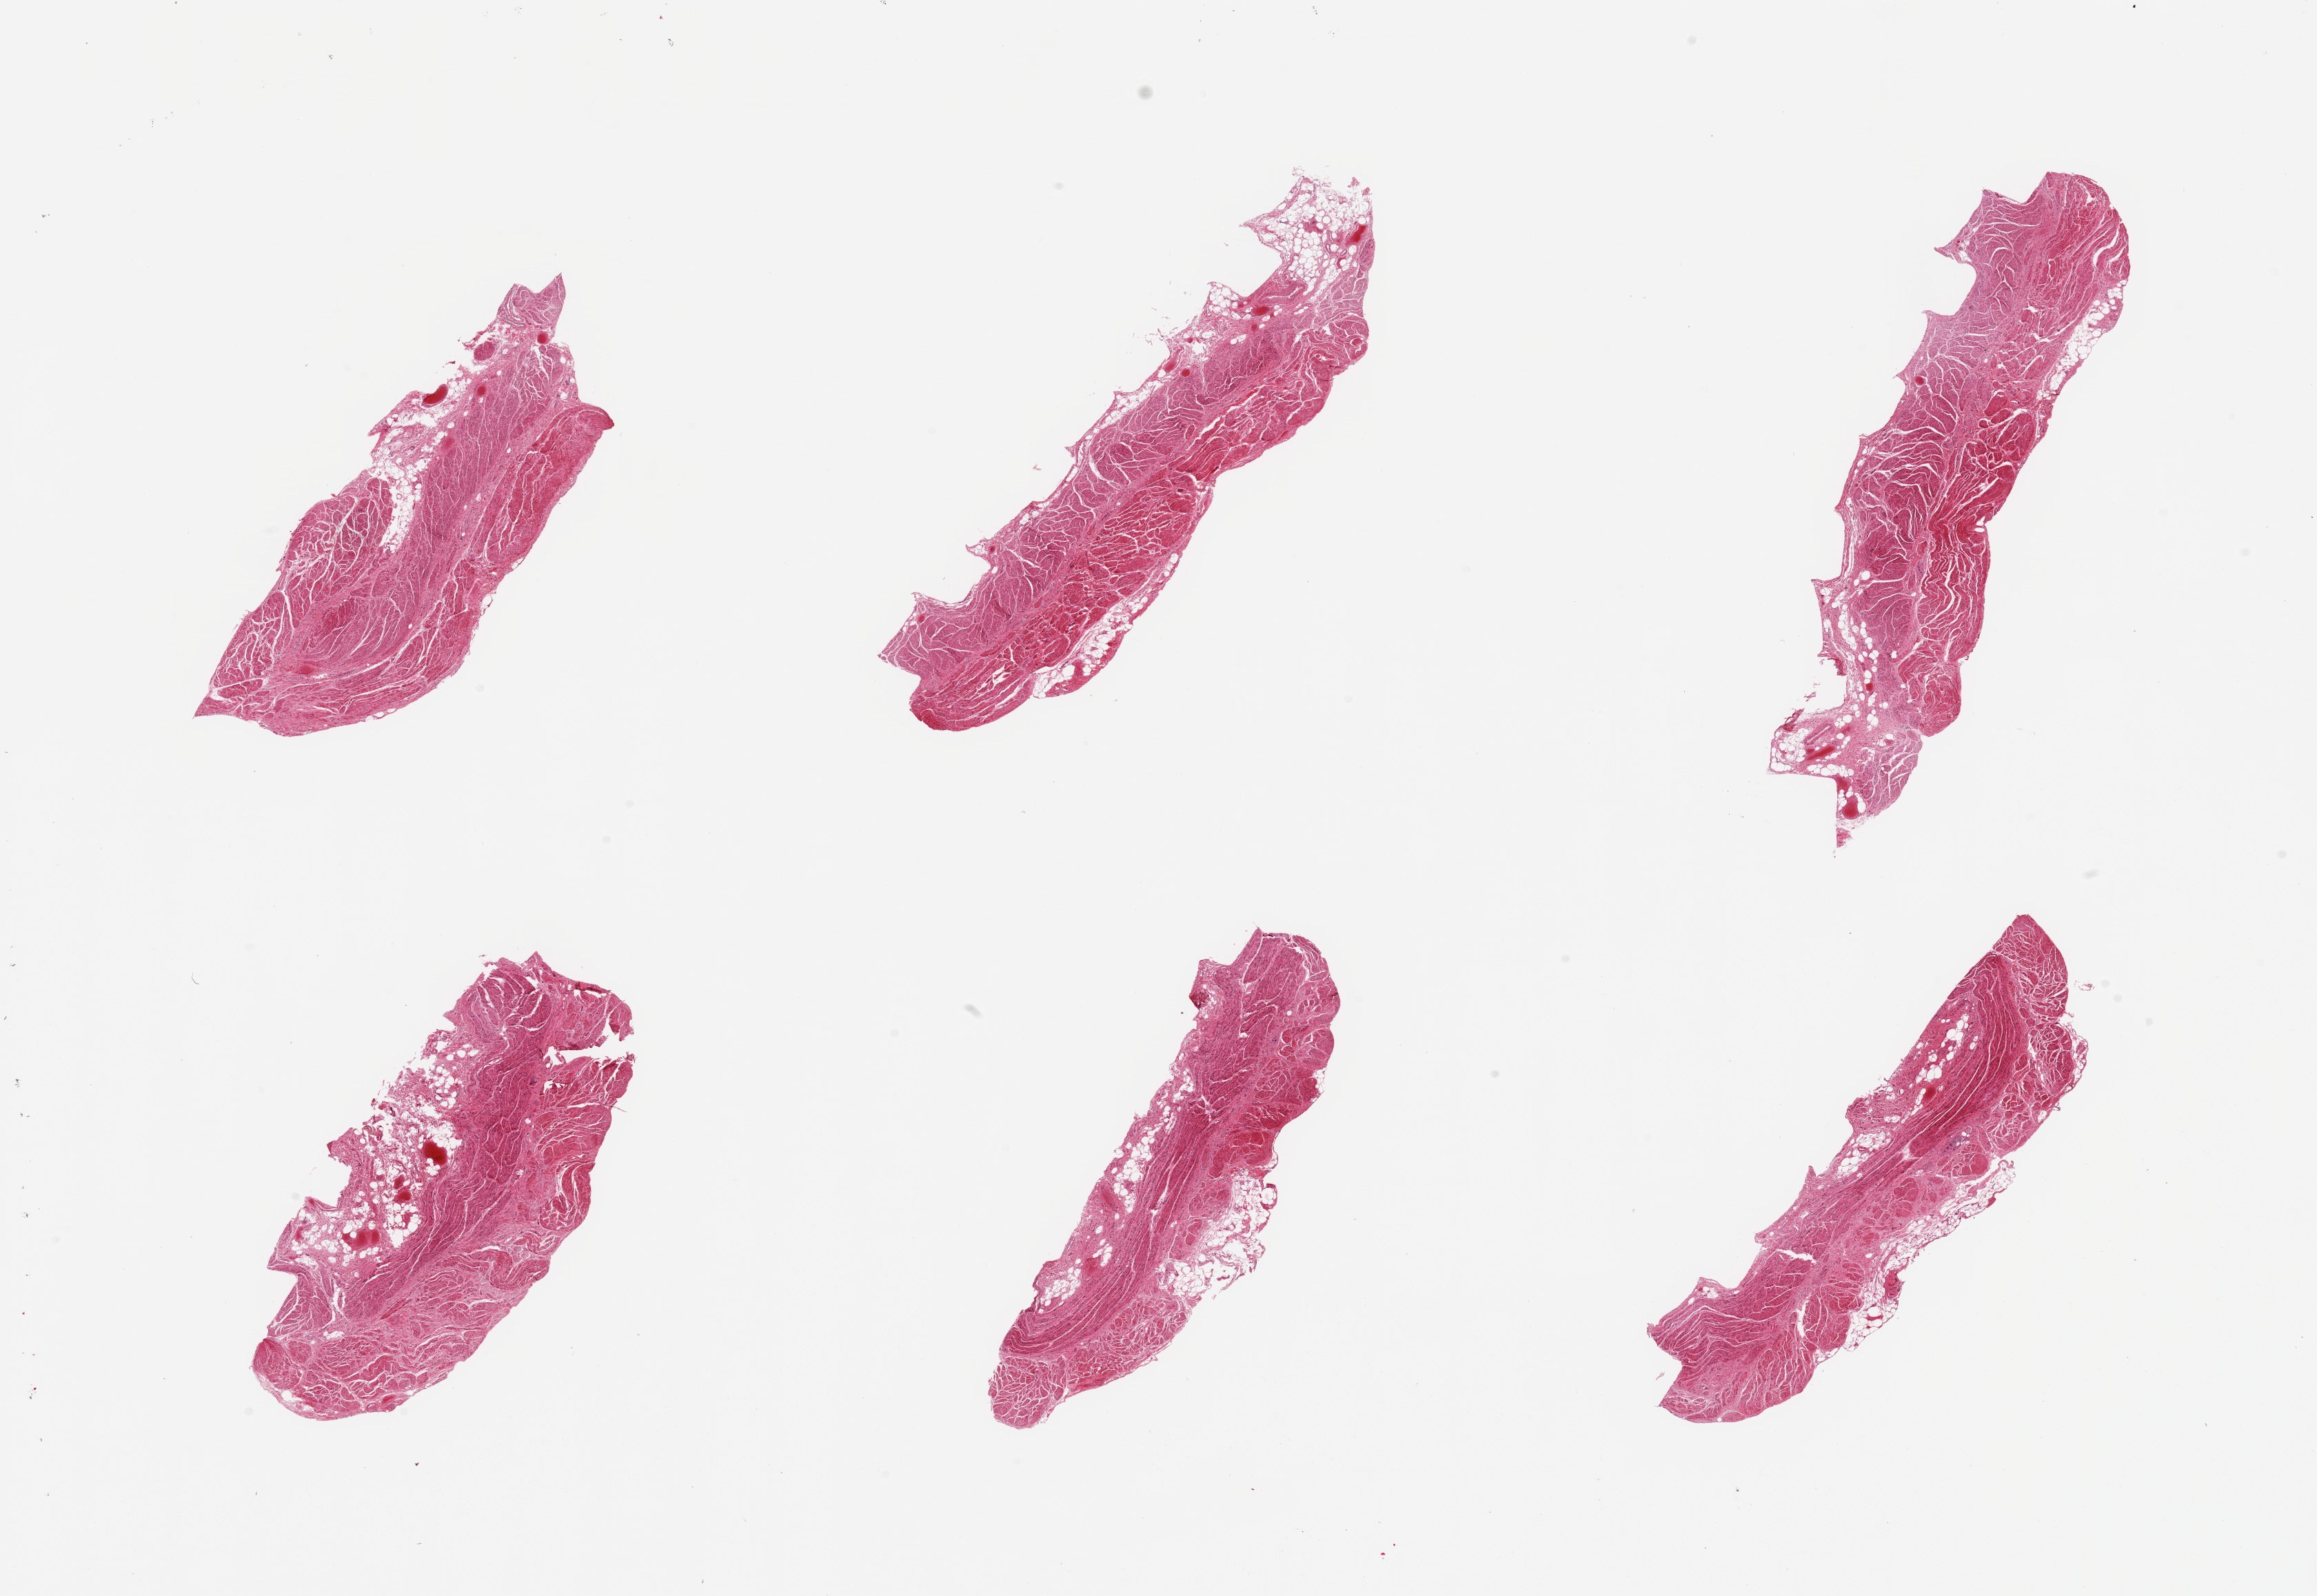
Digitized haematoxylin and eosin-stained section, whole scanned area (about 26.6 x 18.3 mm, acquisition: 20x scan) shown as a low-resolution overview. PAXgene-fixed paraffin-embedded (PFPE) section. Sampled site (target tissue): gastroesophageal junction. Tissue donor sample. Male donor.
Pathologist's review note for this sample: 6 pieces; up to 25% fat content.